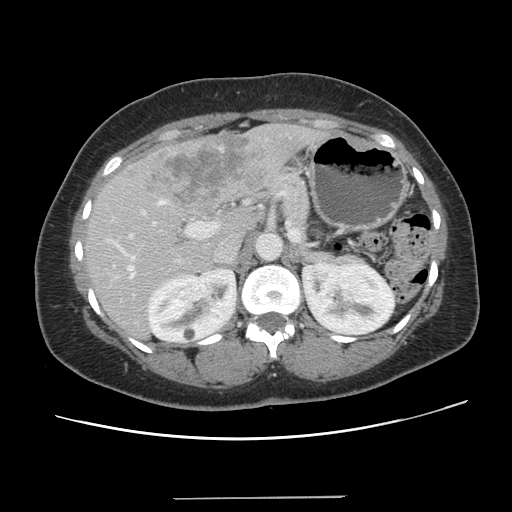
Contrast-enhanced abdominal CT, one axial slice; position 75 of 141 along the scan axis; 120 kVp; intravenous contrast given; soft-tissue window (W 400 / L 40 HU); 2.5 mm slice thickness; 512 × 512 image matrix, field of view 366 × 366 mm. Female patient, age 53 years. From the clinical record (not read from this slice): diagnosis: colorectal cancer liver metastases, imaged before liver resection; multiple liver metastases: no; largest metastasis: 14.5 cm; disease in both lobes: yes.
Outlined on this slice (manually delineated by an expert):
- hepatic veins: bounding box (x1, y1, x2, y2) in pixels: (120, 248, 134, 277)
- liver: (87, 124, 321, 338)
- planned liver remnant (the part of the liver to remain after resection): (87, 205, 256, 338)
- portal vein (with intrahepatic branches): (129, 200, 218, 237)
- liver metastasis: (148, 133, 261, 207)